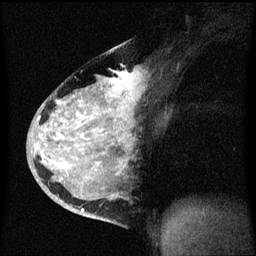
Breast MRI (dynamic contrast-enhanced), one sagittal slice. Slice 37 of 60 in the series (ordered by position). Dynamic contrast-enhanced series, image 2 of 3 at this slice position (ordered by acquisition). 1.5 T. TE 4.2 ms, TR 8.4 ms. 256 × 256 image matrix, field of view 200 × 200 mm. Patient: female, 34 years. Case-level facts recorded for this patient, not image findings: setting: breast cancer imaged before/during neoadjuvant chemotherapy; receptor status: HR-positive, HER2-negative.
Structures marked on this image (semi-automatic segmentation, software-assisted and operator-edited):
- analysis volume of interest (the breast-tissue region the enhancement analysis was run in; not a lesion): bounding box <34,48,141,215> (left, top, right, bottom; pixels)
- tumour enhancement mask (voxels above the 70 % enhancement threshold inside the analysis volume of interest): <38,72,135,211>